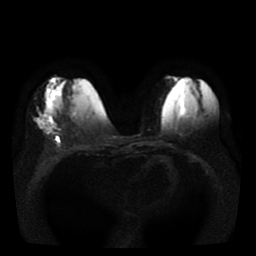
Breast MRI, one axial slice. Position 13 of 41 along the scan axis. Diffusion-weighted series; image 2 of 4 stored at this slice position (different b-values; order by instance number). 1.5 T. 5 mm slice thickness. 256 × 256 image matrix, field of view 330 × 330 mm. Female patient.
Structures marked on this image (expert manual segmentation):
- tumour on diffusion-weighted imaging: bounding box [x1, y1, x2, y2] px = [36, 114, 53, 136]